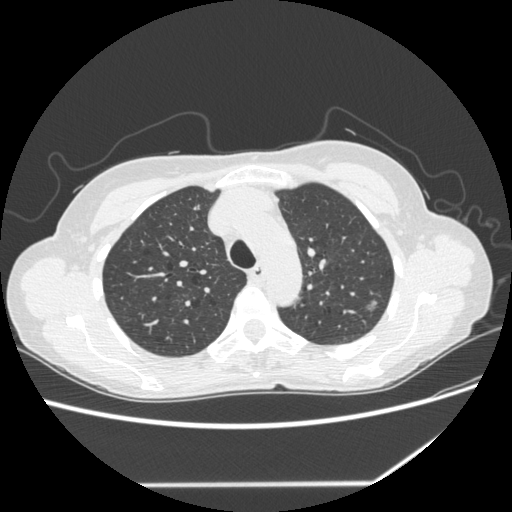
Chest CT (low-dose screening protocol), one axial image, second screening round (one year after baseline), lung window (W 1500 / L -600 HU), 1.25 mm slice thickness, standard (soft-tissue) reconstruction kernel (STANDARD), slice 58 of 255 in the series. Female participant, aged 61 years at enrolment. Former smoker at enrolment.
Lesion marked by an expert reader, bounding box (x1, y1, x2, y2) in pixels: (355, 293, 388, 321). Reader record for this screening exam (exam-level; its link to the box is not recorded): non-calcified nodule or mass ≥4 mm, left upper lobe, 8 × 7 mm, poorly defined margins, mixed attenuation, pre-existing on the prior screen: yes; interval growth: yes. Participant outcome: lung cancer diagnosed 113 days after this screen — bronchiolo-alveolar adenocarcinoma, NOS, left upper lobe, well differentiated (G1), stage IA (AJCC 6th edition), 8 mm at pathology.